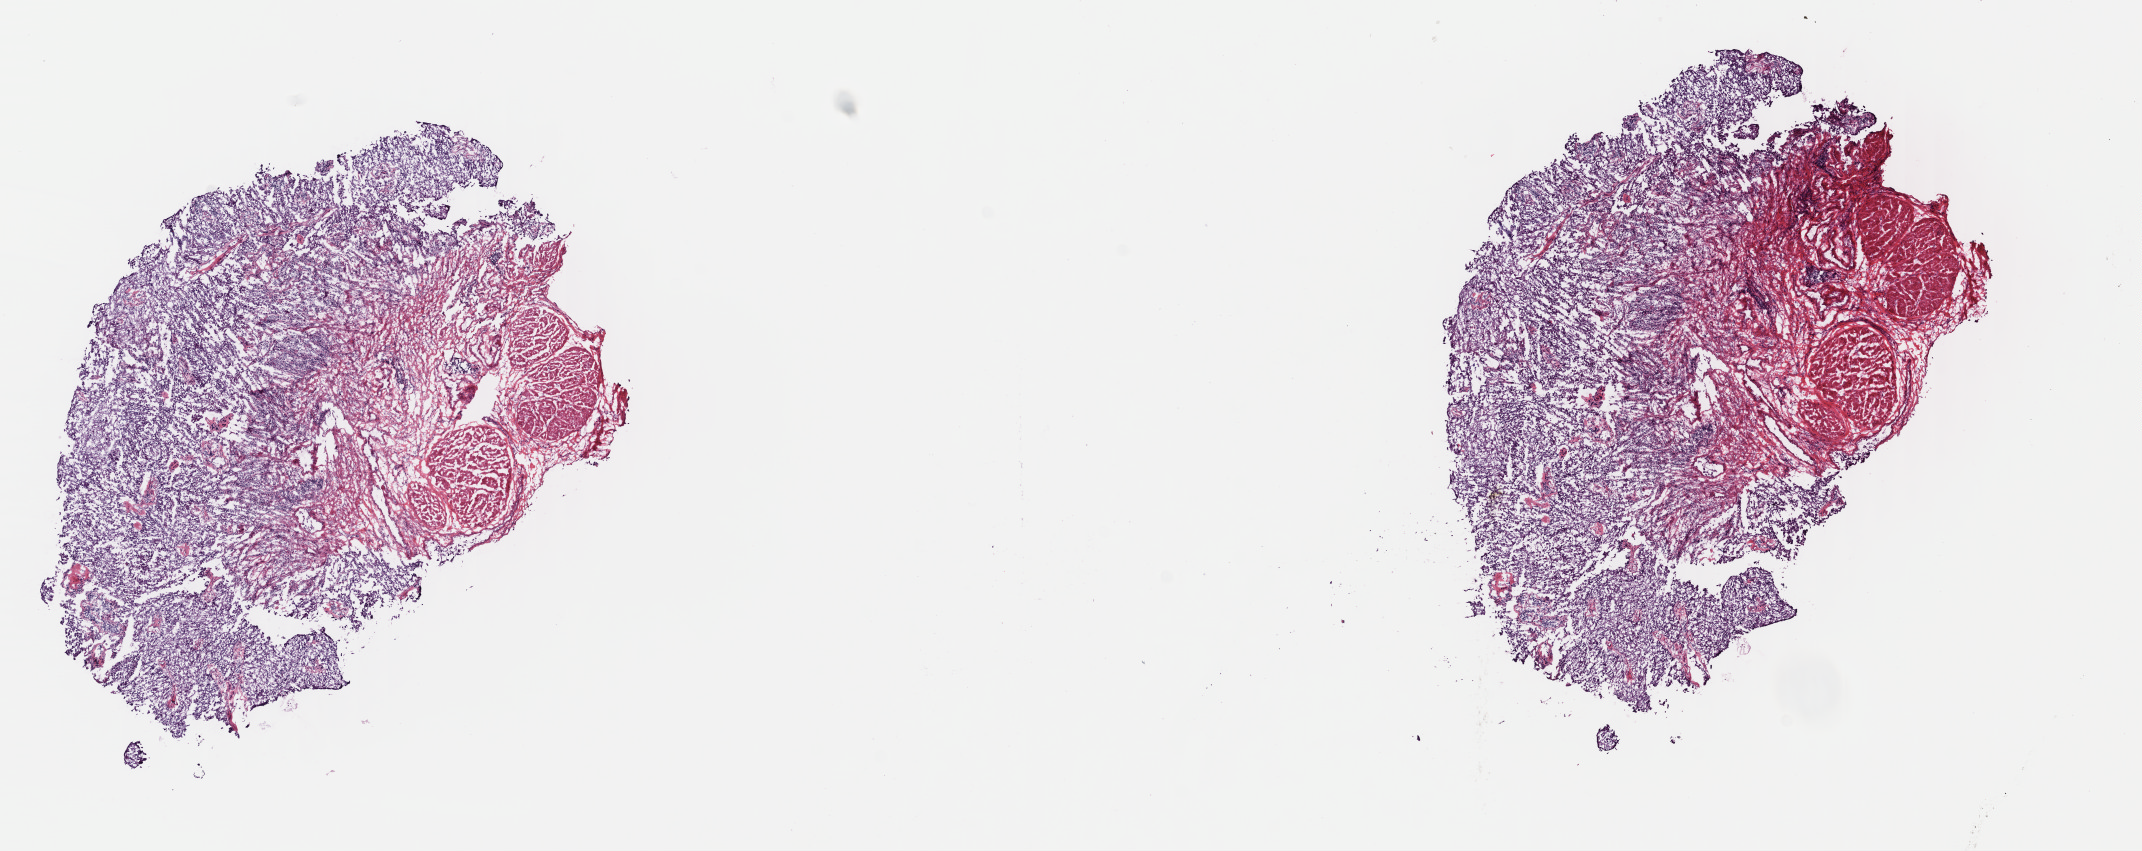
Digitized H&E-stained tissue section (whole slide) — low-resolution overview of the scanned area, about 16.8 x 6.7 mm; frozen section; bladder, primary tumour sample. Female, age 86 years at initial diagnosis. Histologic grade: high grade. Composition of this section per pathologist review: tumour cells 70%, tumour nuclei 80%, normal cells 0%, stromal cells 30%, necrosis 0%. Infiltration values recorded for this section: lymphocyte infiltration 0%, monocyte infiltration 0%, neutrophil infiltration 0%.
Pathologic diagnosis: Transitional cell carcinoma. Lymph nodes positive (case pathology): 0 of 22 examined. AJCC pathologic stage: II (7th edition).